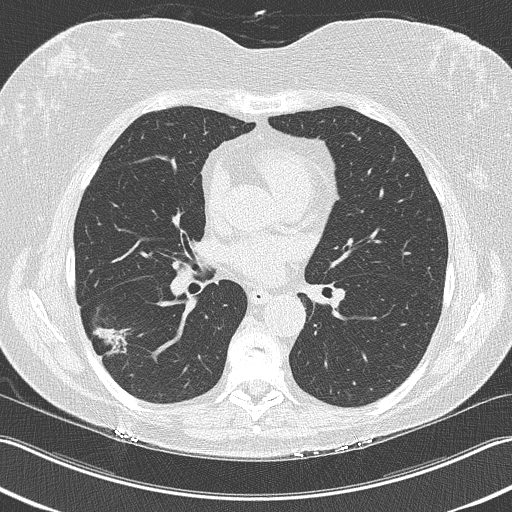
Low-dose screening chest CT, one axial slice; slice 118 of 210 in the series (ordered by position); 120 kVp; lung window (W 1500 / L -600 HU); 2 mm slice thickness; 512 × 512 image matrix.
Outlined on this slice (outlined manually by an expert reader):
- lesion 1 (tumor, lower lobe of right lung): bounding box (x1, y1, x2, y2) in pixels: (93, 327, 131, 356)